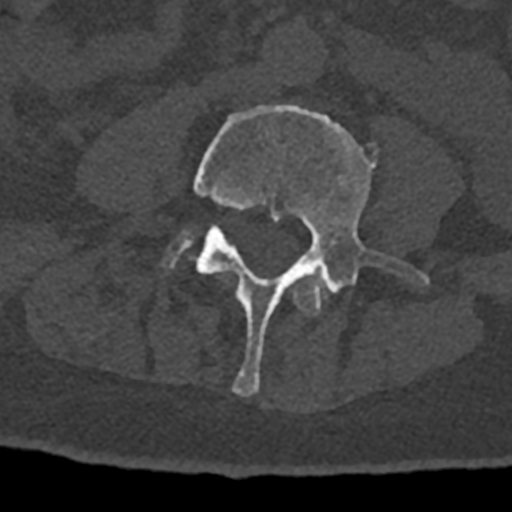
CT including the spine, one axial slice; position 261 of 797 along the scan axis; reconstruction kernel Br40s/3; bone window (W 1800 / L 400 HU); 0.5 mm slice thickness; 512 × 512 image matrix, field of view 160 × 160 mm. Male patient, age 74 years. Case-level facts recorded for this patient, not image findings: primary cancer: renal.
Structures marked on this image (semi-automatic segmentation, software-assisted and operator-edited):
- L3 vertebra: bounding box <293,274,328,315> (left, top, right, bottom; pixels)
- L4 vertebra: <193,105,429,396>
- L5 vertebra: <166,232,191,268>